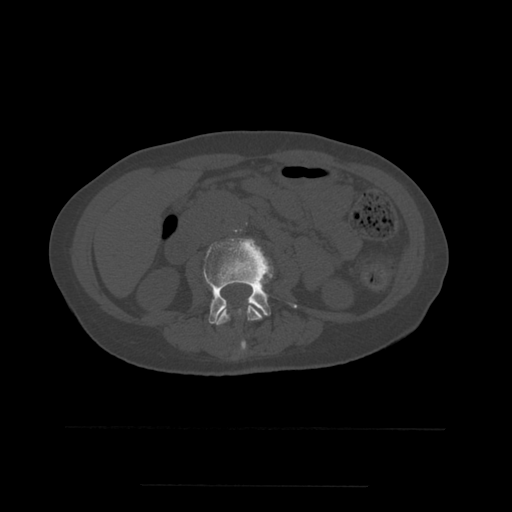
CT including the spine, one axial slice; position 196 of 544 along the scan axis; bone window (W 1800 / L 400 HU); 1.25 mm slice thickness; 512 × 512 image matrix, field of view 350 × 350 mm. Patient age 58 years. Case-level facts recorded for this patient, not image findings: primary cancer: lung.
Structures marked on this image (semi-automatically segmented with operator editing):
- L2 vertebra: box from (x=216, y=302) to (x=263, y=350) px
- L3 vertebra: (x=203, y=238)–(x=297, y=324)